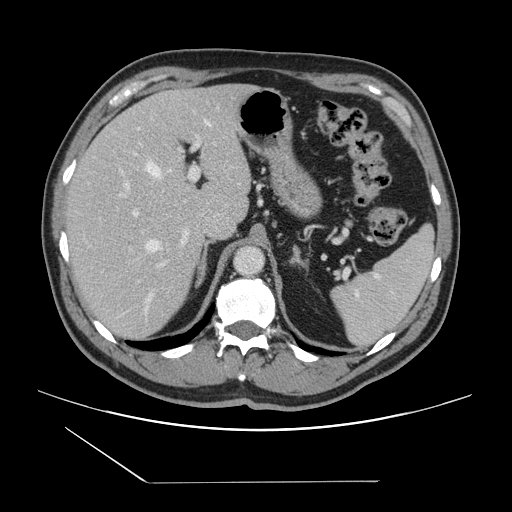
Contrast-enhanced abdominal CT, one axial slice; intravenous contrast given; soft-tissue window (W 400 / L 40 HU); 2.5 mm slice thickness; 512 × 512 image matrix, field of view 407 × 407 mm. Male patient, age 61 years. From the clinical record (not read from this slice): diagnosis: colorectal cancer liver metastases, imaged before liver resection; multiple liver metastases: yes; largest metastasis: 5.5 cm; disease in both lobes: yes.
Structures marked on this image (expert manual segmentation):
- hepatic veins: box from (x=147, y=121) to (x=211, y=300) px
- liver: (x=66, y=85)–(x=251, y=341)
- planned liver remnant (the part of the liver to remain after resection): (x=68, y=85)–(x=238, y=223)
- portal vein (with intrahepatic branches): (x=90, y=135)–(x=200, y=265)